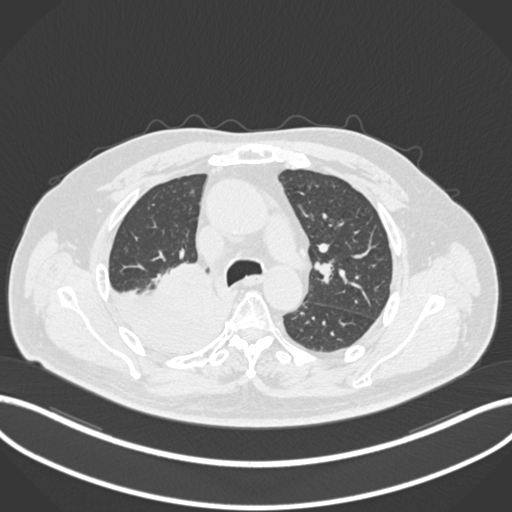
Chest CT, one axial slice. Slice 136 of 218 in the series (ordered by position). Reconstruction kernel B30f. Lung window (W 1500 / L -600 HU). 512 × 512 image matrix. Patient: male, 68 years. Case-level facts recorded for this patient, not image findings: clinical TNM (as recorded): T2a N0 M0.
Outlined on this slice (bounding box drawn by a radiologist):
- lung tumour (recorded histology: adenocarcinoma): box from (x=109, y=263) to (x=228, y=355) px